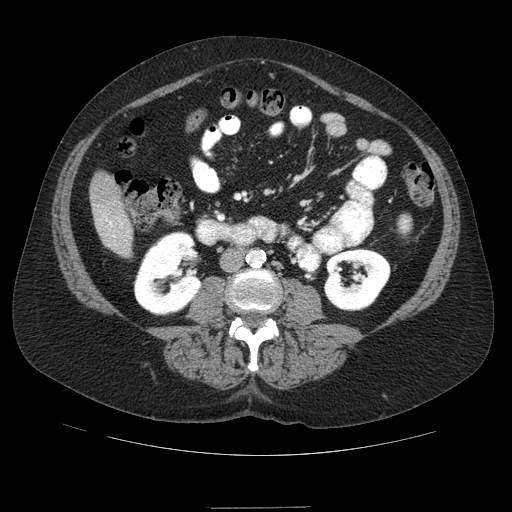
Contrast-enhanced abdominal CT (liver protocol), one axial slice. Slice 16 of 89 in the series (ordered by position). Soft-tissue window (W 400 / L 40 HU). 2.5 mm slice thickness. 512 × 512 image matrix, field of view 400 × 400 mm. From the clinical record (not read from this slice): diagnosis: hepatocellular carcinoma (patient treated with transarterial chemoembolisation; whether this scan precedes or follows treatment is not stated here); TNM stage (as recorded): Stage-IIIB; Child-Pugh class: A.
Annotated regions visible in this slice (semi-automatically segmented with operator editing):
- liver parenchyma outside the tumour (the mass and vessels are separate outlines, so this box may not span the whole liver): bounding box <90,172,132,256> (left, top, right, bottom; pixels)
- liver vessels: <105,218,115,237>